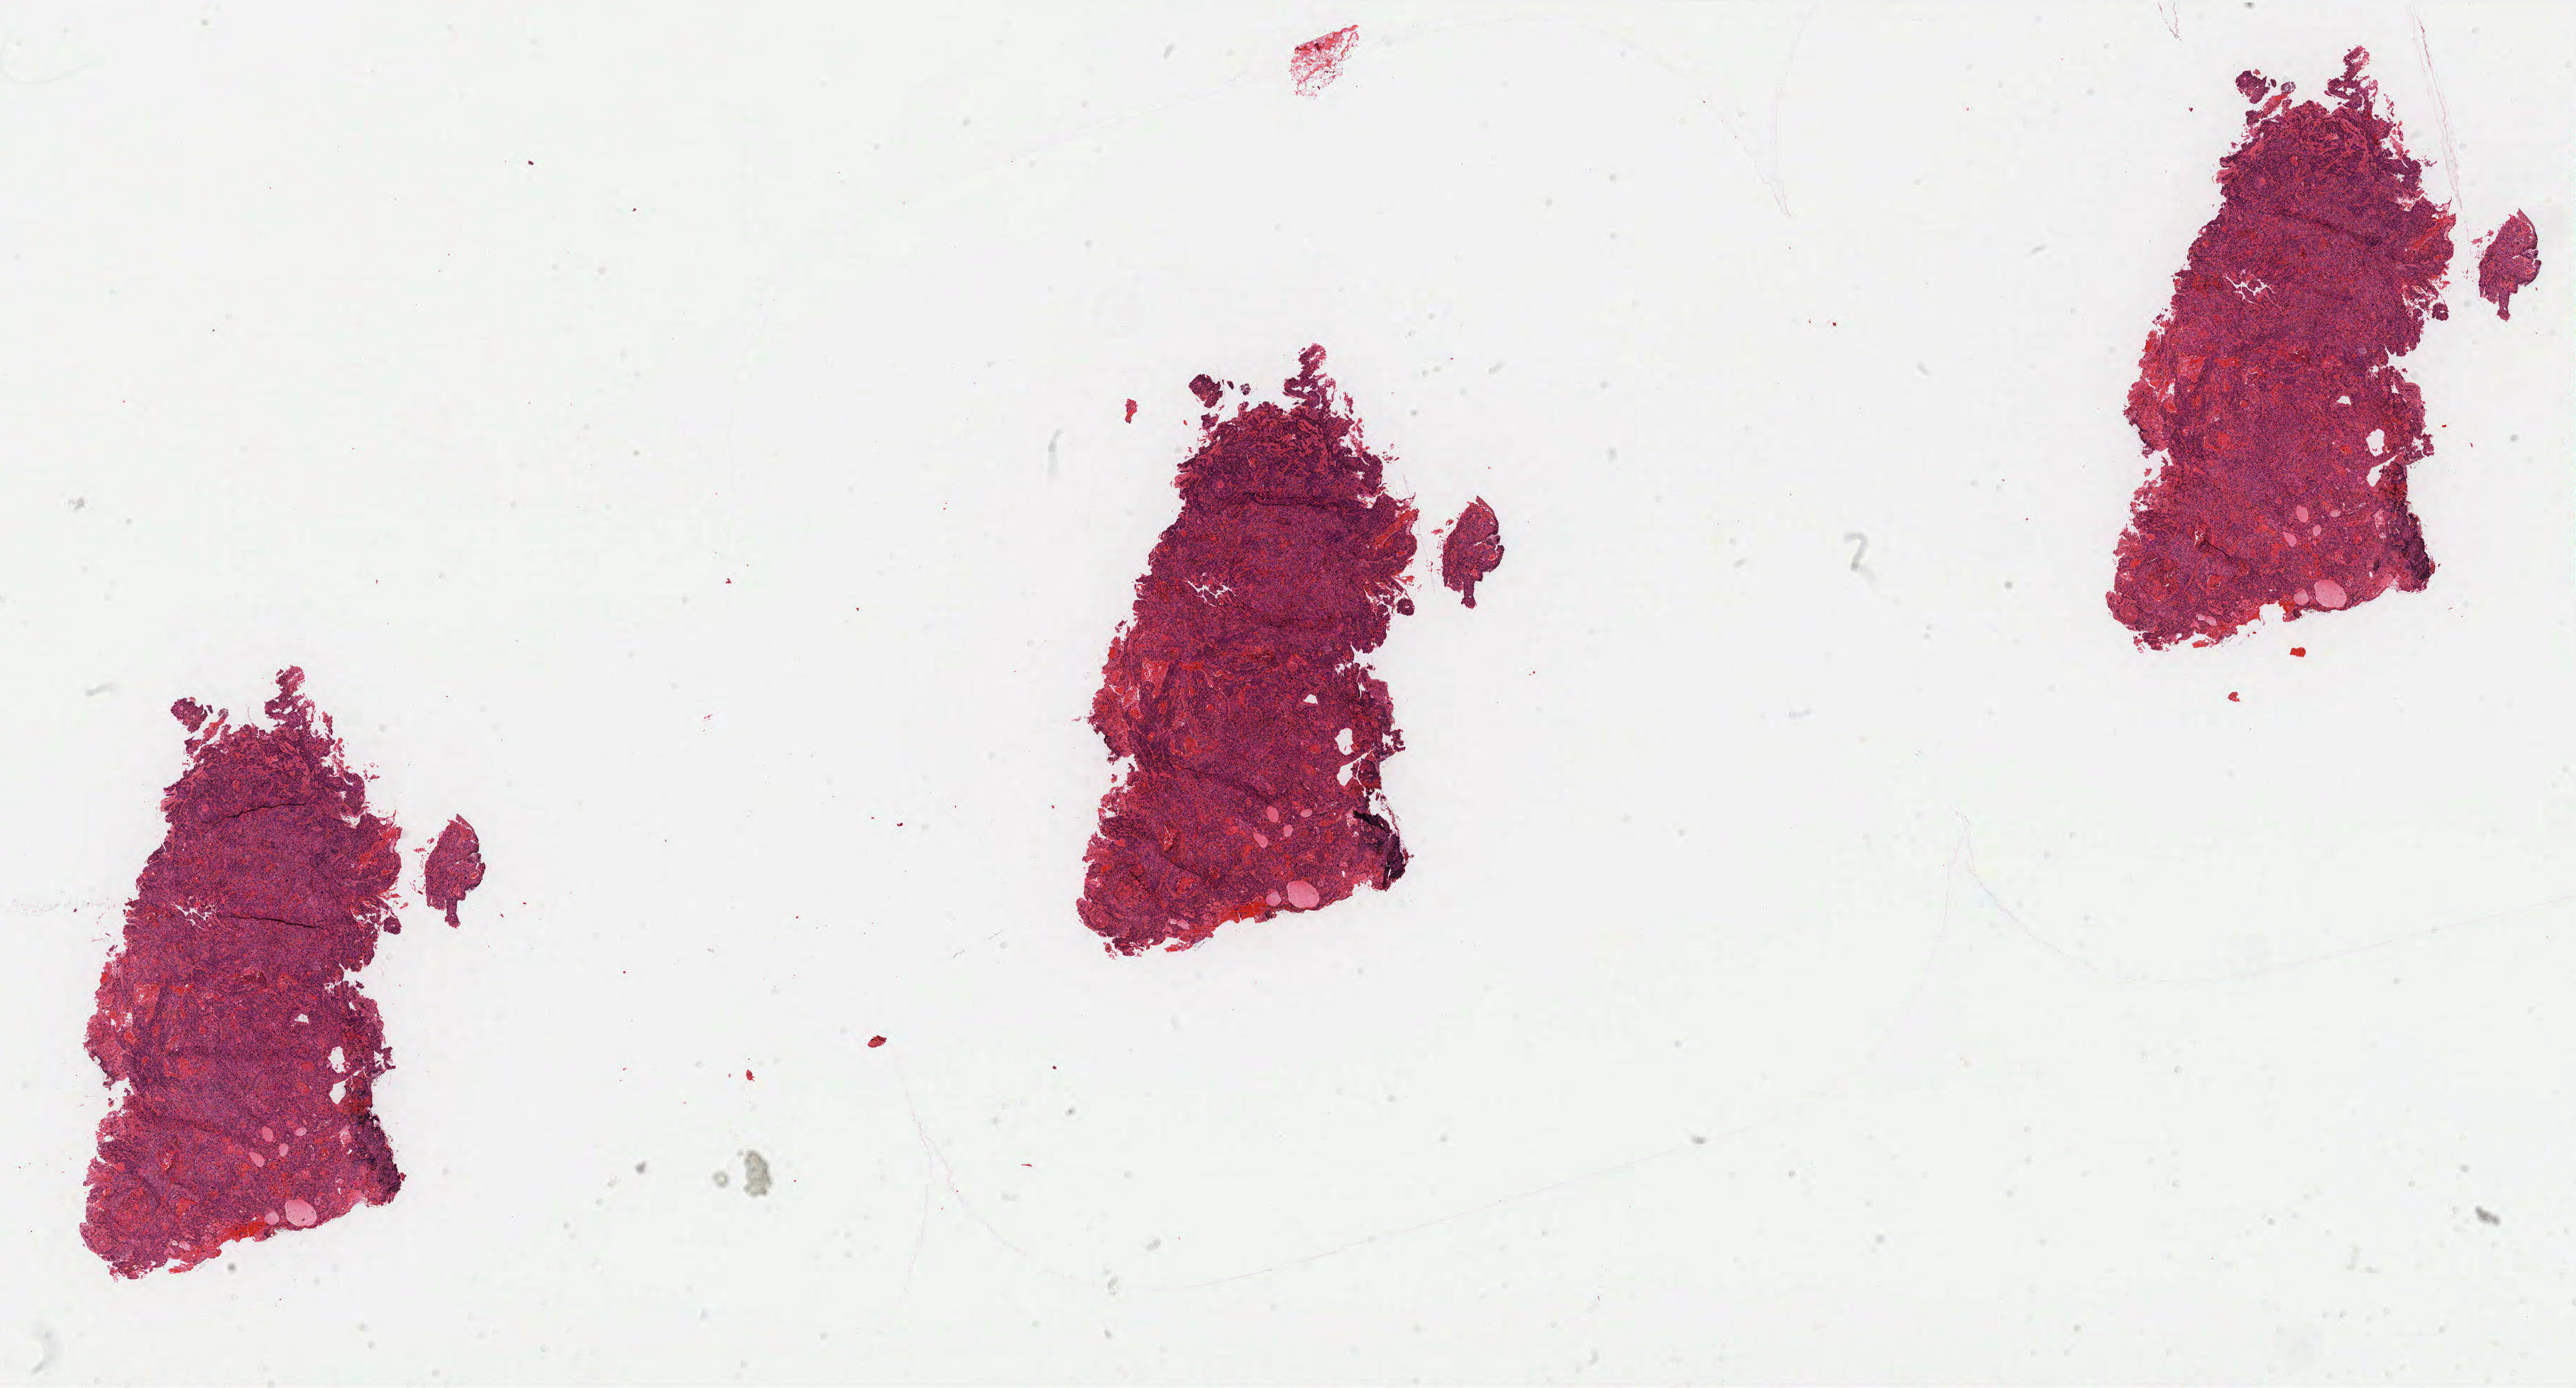
H&E whole-slide image, whole scanned area (about 29.1 x 15.7 mm) shown as a low-resolution overview, FFPE section, sample: primary tumour, cervix. Patient: female, age at initial diagnosis 43 years. Histologic grade: G2 (moderately differentiated).
Diagnosis: Squamous cell carcinoma, NOS. FIGO stage: IIB.